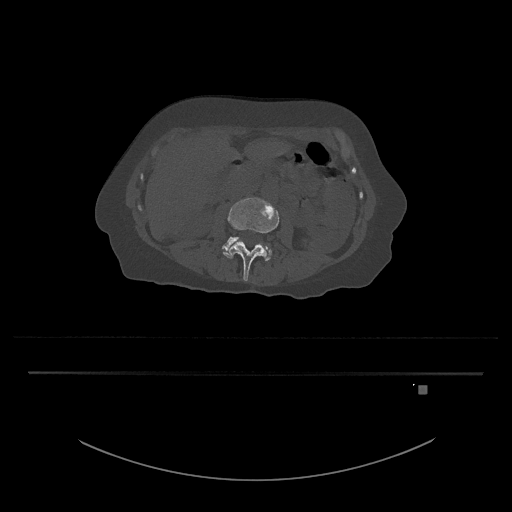
CT including the spine, one axial slice. Slice 411 of 797 in the series (ordered by position). Bone window (W 1800 / L 400 HU). 512 × 512 image matrix, field of view 500 × 500 mm. Patient: female, 57 years. From the clinical record (not read from this slice): primary cancer: cervical.
Outlined on this slice (semi-automatic segmentation, software-assisted and operator-edited):
- L3 vertebra: bounding box [x1, y1, x2, y2] px = [223, 197, 279, 281]
- L4 vertebra: [222, 236, 272, 261]